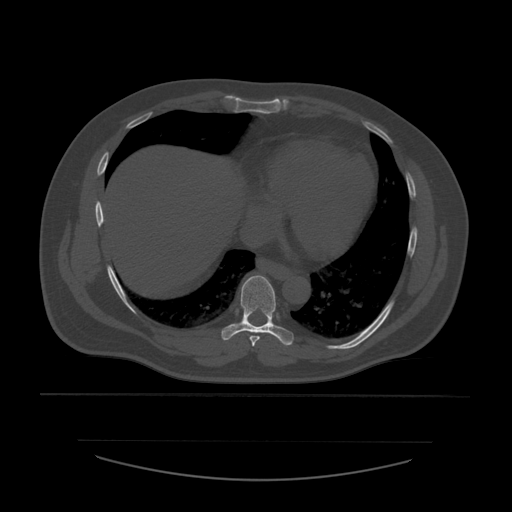
CT including the spine, one axial slice. Slice 340 of 532 in the series (ordered by position). Reconstruction kernel STANDARD. 120 kVp. Bone window (W 1800 / L 400 HU). 1.25 mm slice thickness. 512 × 512 image matrix. Patient age 44 years. Case-level facts recorded for this patient, not image findings: primary cancer: soft tissue sarcoma.
Structures marked on this image (semi-automatic segmentation, software-assisted and operator-edited):
- T7 vertebra: box from (x=249, y=336) to (x=260, y=347) px
- T8 vertebra: (x=221, y=276)–(x=294, y=346)